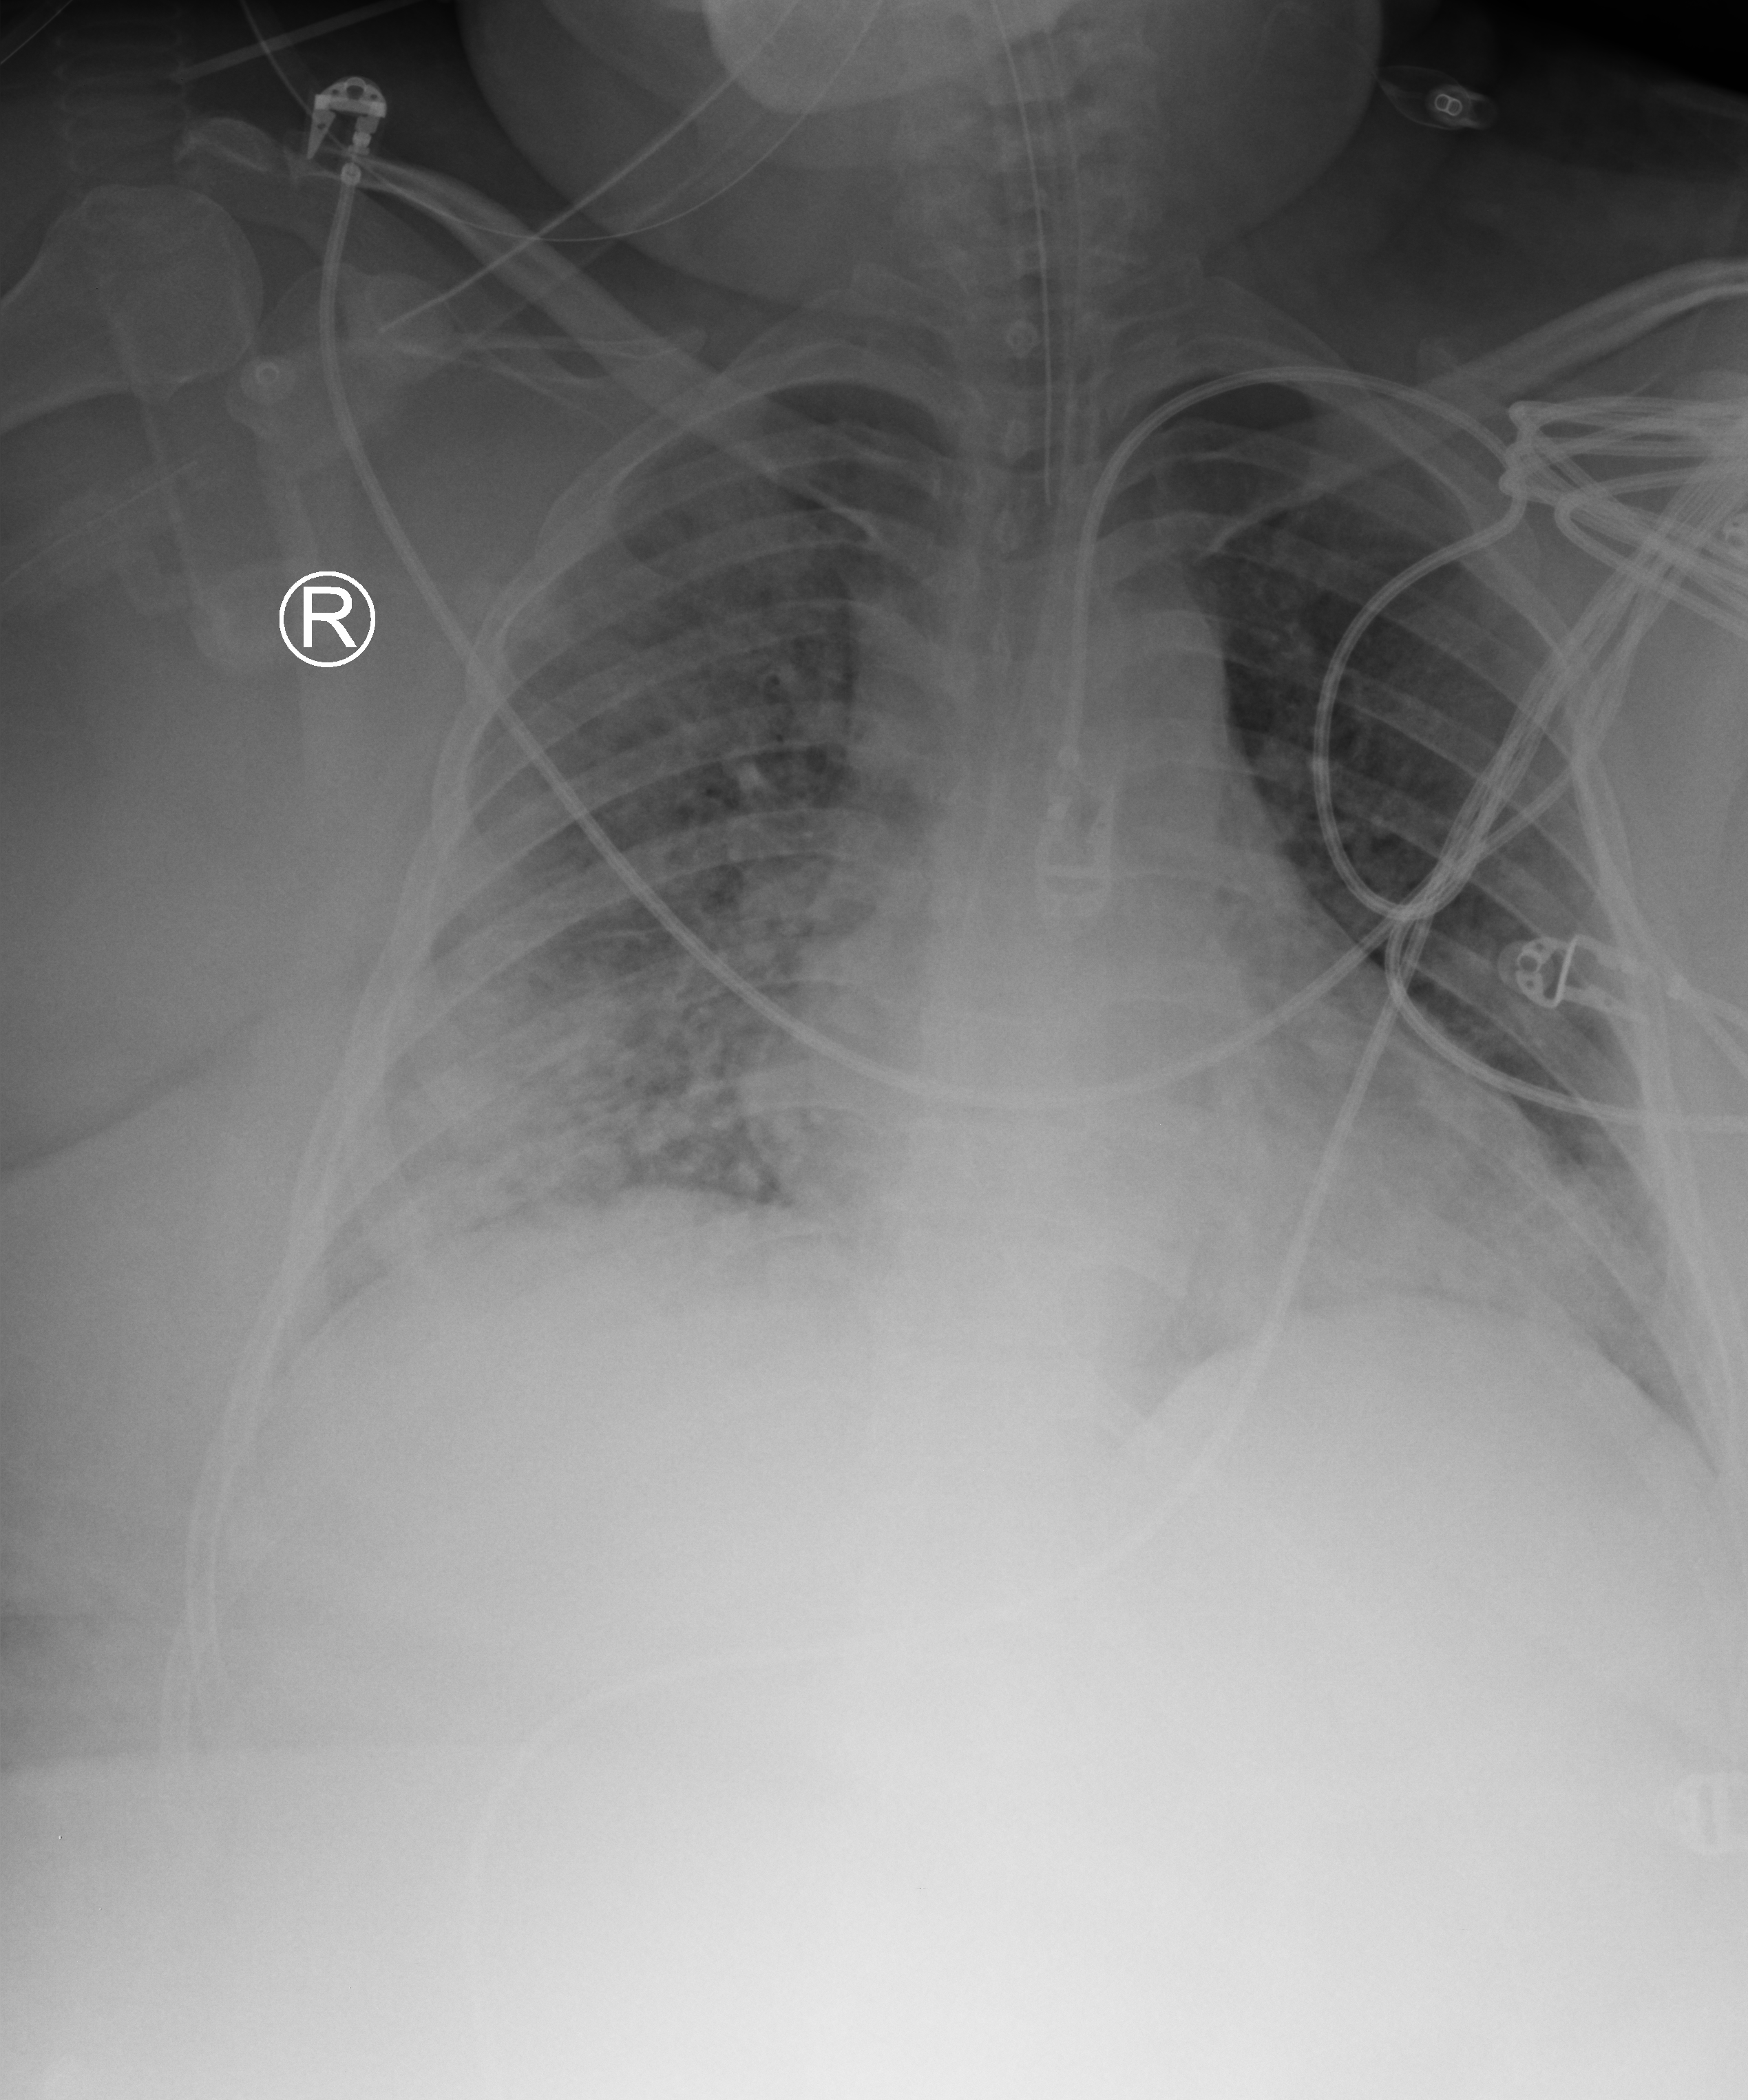
Portable chest radiograph; anteroposterior (AP) projection. Female patient hospitalised with COVID-19, age 18–59 years.
Admission-level facts for this patient (not findings on this image; timing relative to this image not recorded): mechanically ventilated during this hospital stay: yes; admitted to intensive care during this hospital stay: yes; hypertension (admission record): no.